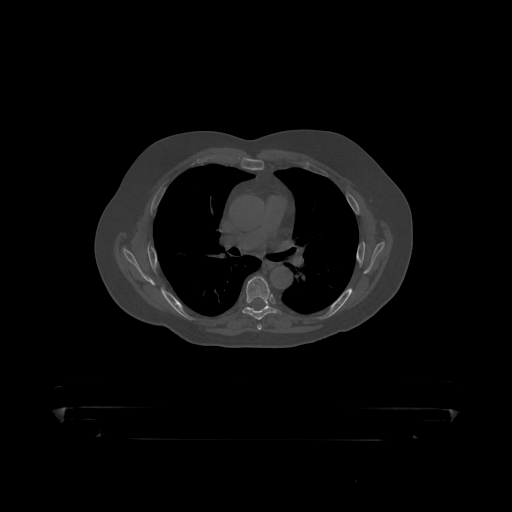
CT including the spine, one axial slice. Position 301 of 390 along the scan axis. Reconstruction kernel STANDARD. Bone window (W 1800 / L 400 HU). 1.25 mm slice thickness. 512 × 512 image matrix, field of view 650 × 650 mm. Patient: male, 60 years. Case-level facts recorded for this patient, not image findings: primary cancer: prostate.
Structures marked on this image (semi-automatically segmented with operator editing):
- T6 vertebra: box from (x=243, y=277) to (x=279, y=319) px